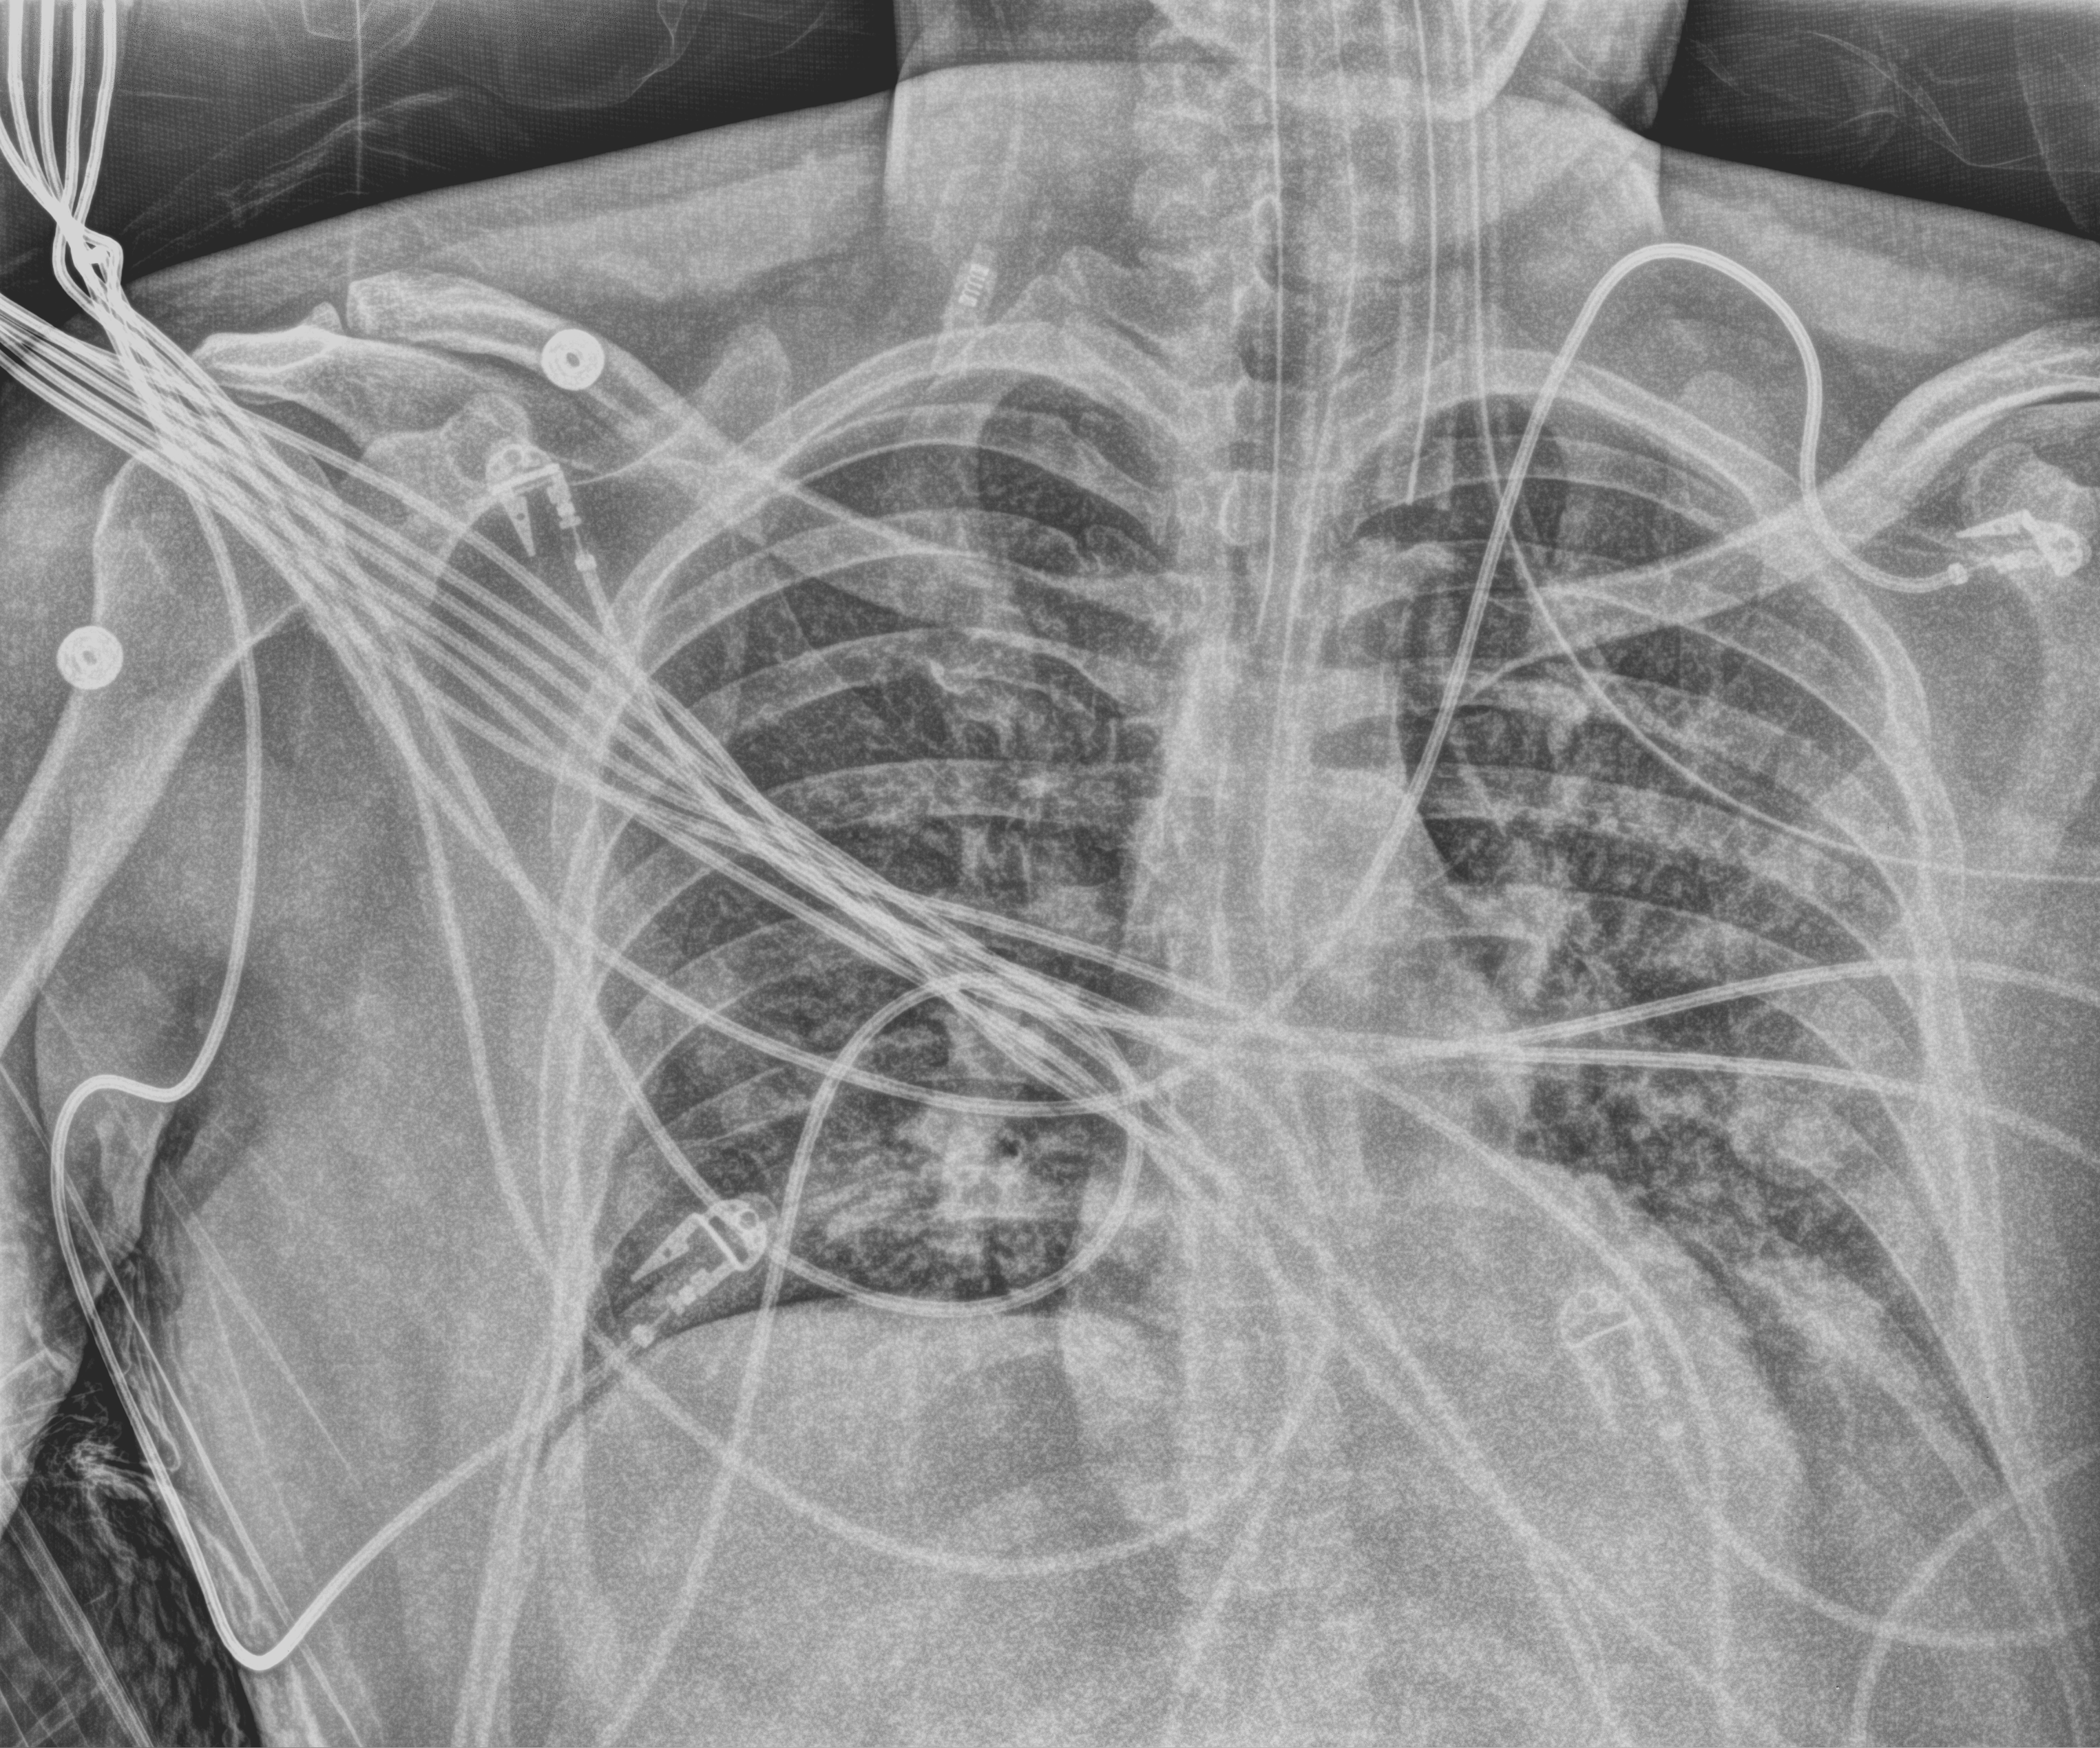
Portable chest radiograph; anteroposterior (AP) projection. Male patient hospitalised with COVID-19, age 18–59 years.
From the hospital-stay record, not from the radiograph (when in the stay this image was taken is not recorded): length of hospital stay: 22 days; mechanically ventilated during this hospital stay: yes.